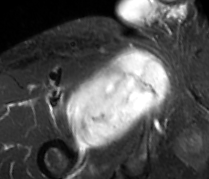
MRI of an extremity soft-tissue mass, one axial slice; slice 63 of 89 in the series (ordered by position); STIR; MR volume resampled by the dataset authors to the PET/CT grid (not the native acquisition matrix); 3.27 mm slice thickness; 209 × 179 image matrix. Male patient. Case-level facts recorded for this patient, not image findings: histological type: undifferentiated - pleiomorphic; grade: high; site of the primary tumour: right thigh.
Outlined on this slice (expert contour drawn on MRI and transferred to this co-registered scan by the dataset authors):
- gross tumour volume including surrounding oedema: bounding box <66,48,168,150> (left, top, right, bottom; pixels)
- gross tumour volume (mass): <66,48,168,150>